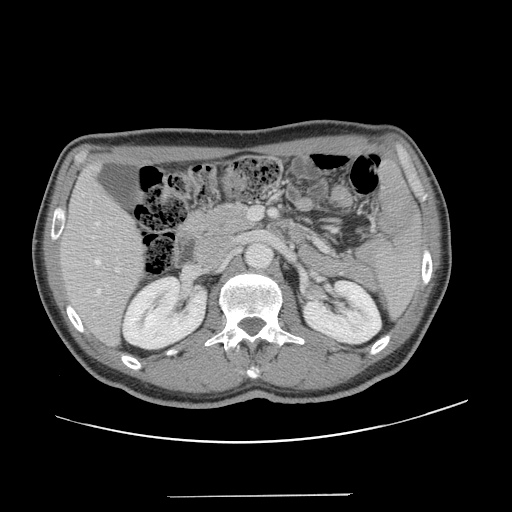
Contrast-enhanced abdominal CT, one axial slice. Slice 67 of 131 in the series (ordered by position). 120 kVp. Intravenous contrast given. Soft-tissue window (W 400 / L 40 HU). 2.5 mm slice thickness. 512 × 512 image matrix, field of view 403 × 403 mm. Male patient, age 60 years. Case-level facts recorded for this patient, not image findings: diagnosis: colorectal cancer liver metastases, imaged before liver resection; multiple liver metastases: no; largest metastasis: 2.5 cm; disease in both lobes: no.
Outlined on this slice (expert manual segmentation):
- hepatic veins: bounding box (x1, y1, x2, y2) in pixels: (96, 222, 101, 295)
- liver: (61, 168, 145, 345)
- planned liver remnant (the part of the liver to remain after resection): (61, 168, 145, 345)